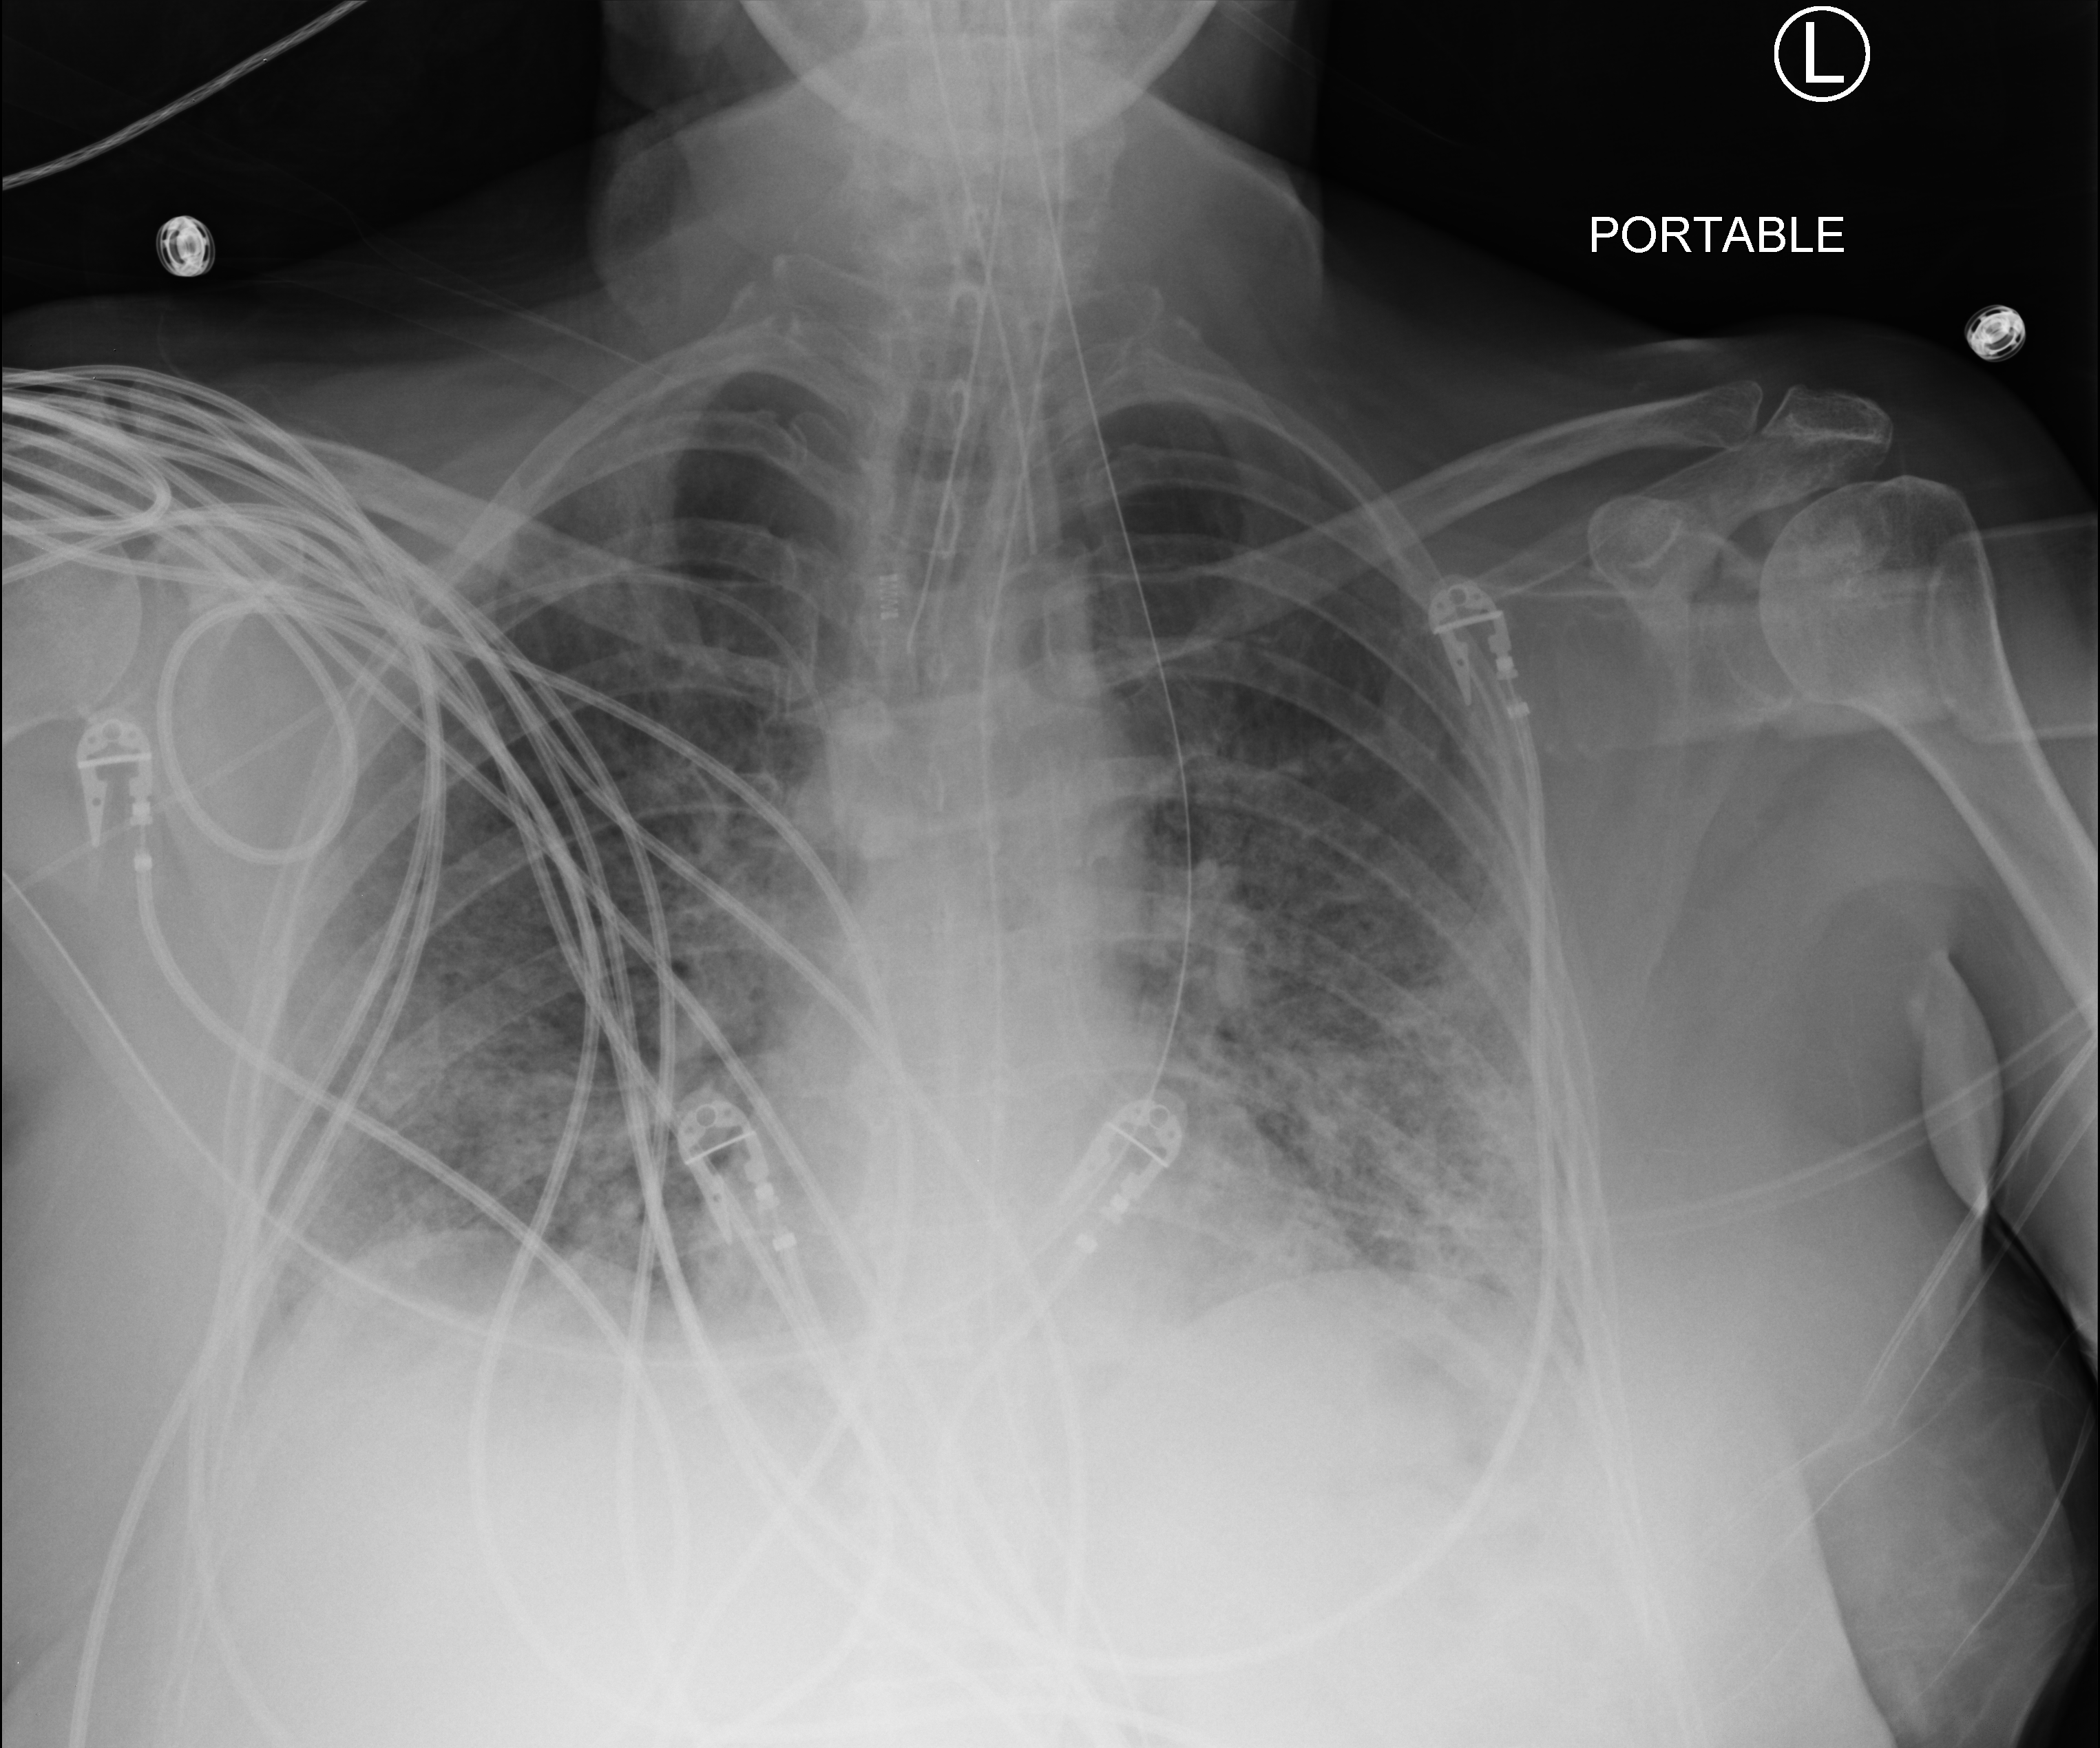
Bedside chest radiograph (computed radiography). Female patient hospitalised with COVID-19, age 60–74 years.
Hospital-stay facts (about this admission, not read from this image; timing relative to this image not recorded):
- mechanically ventilated during this hospital stay: yes
- other chronic lung disease (admission record): no